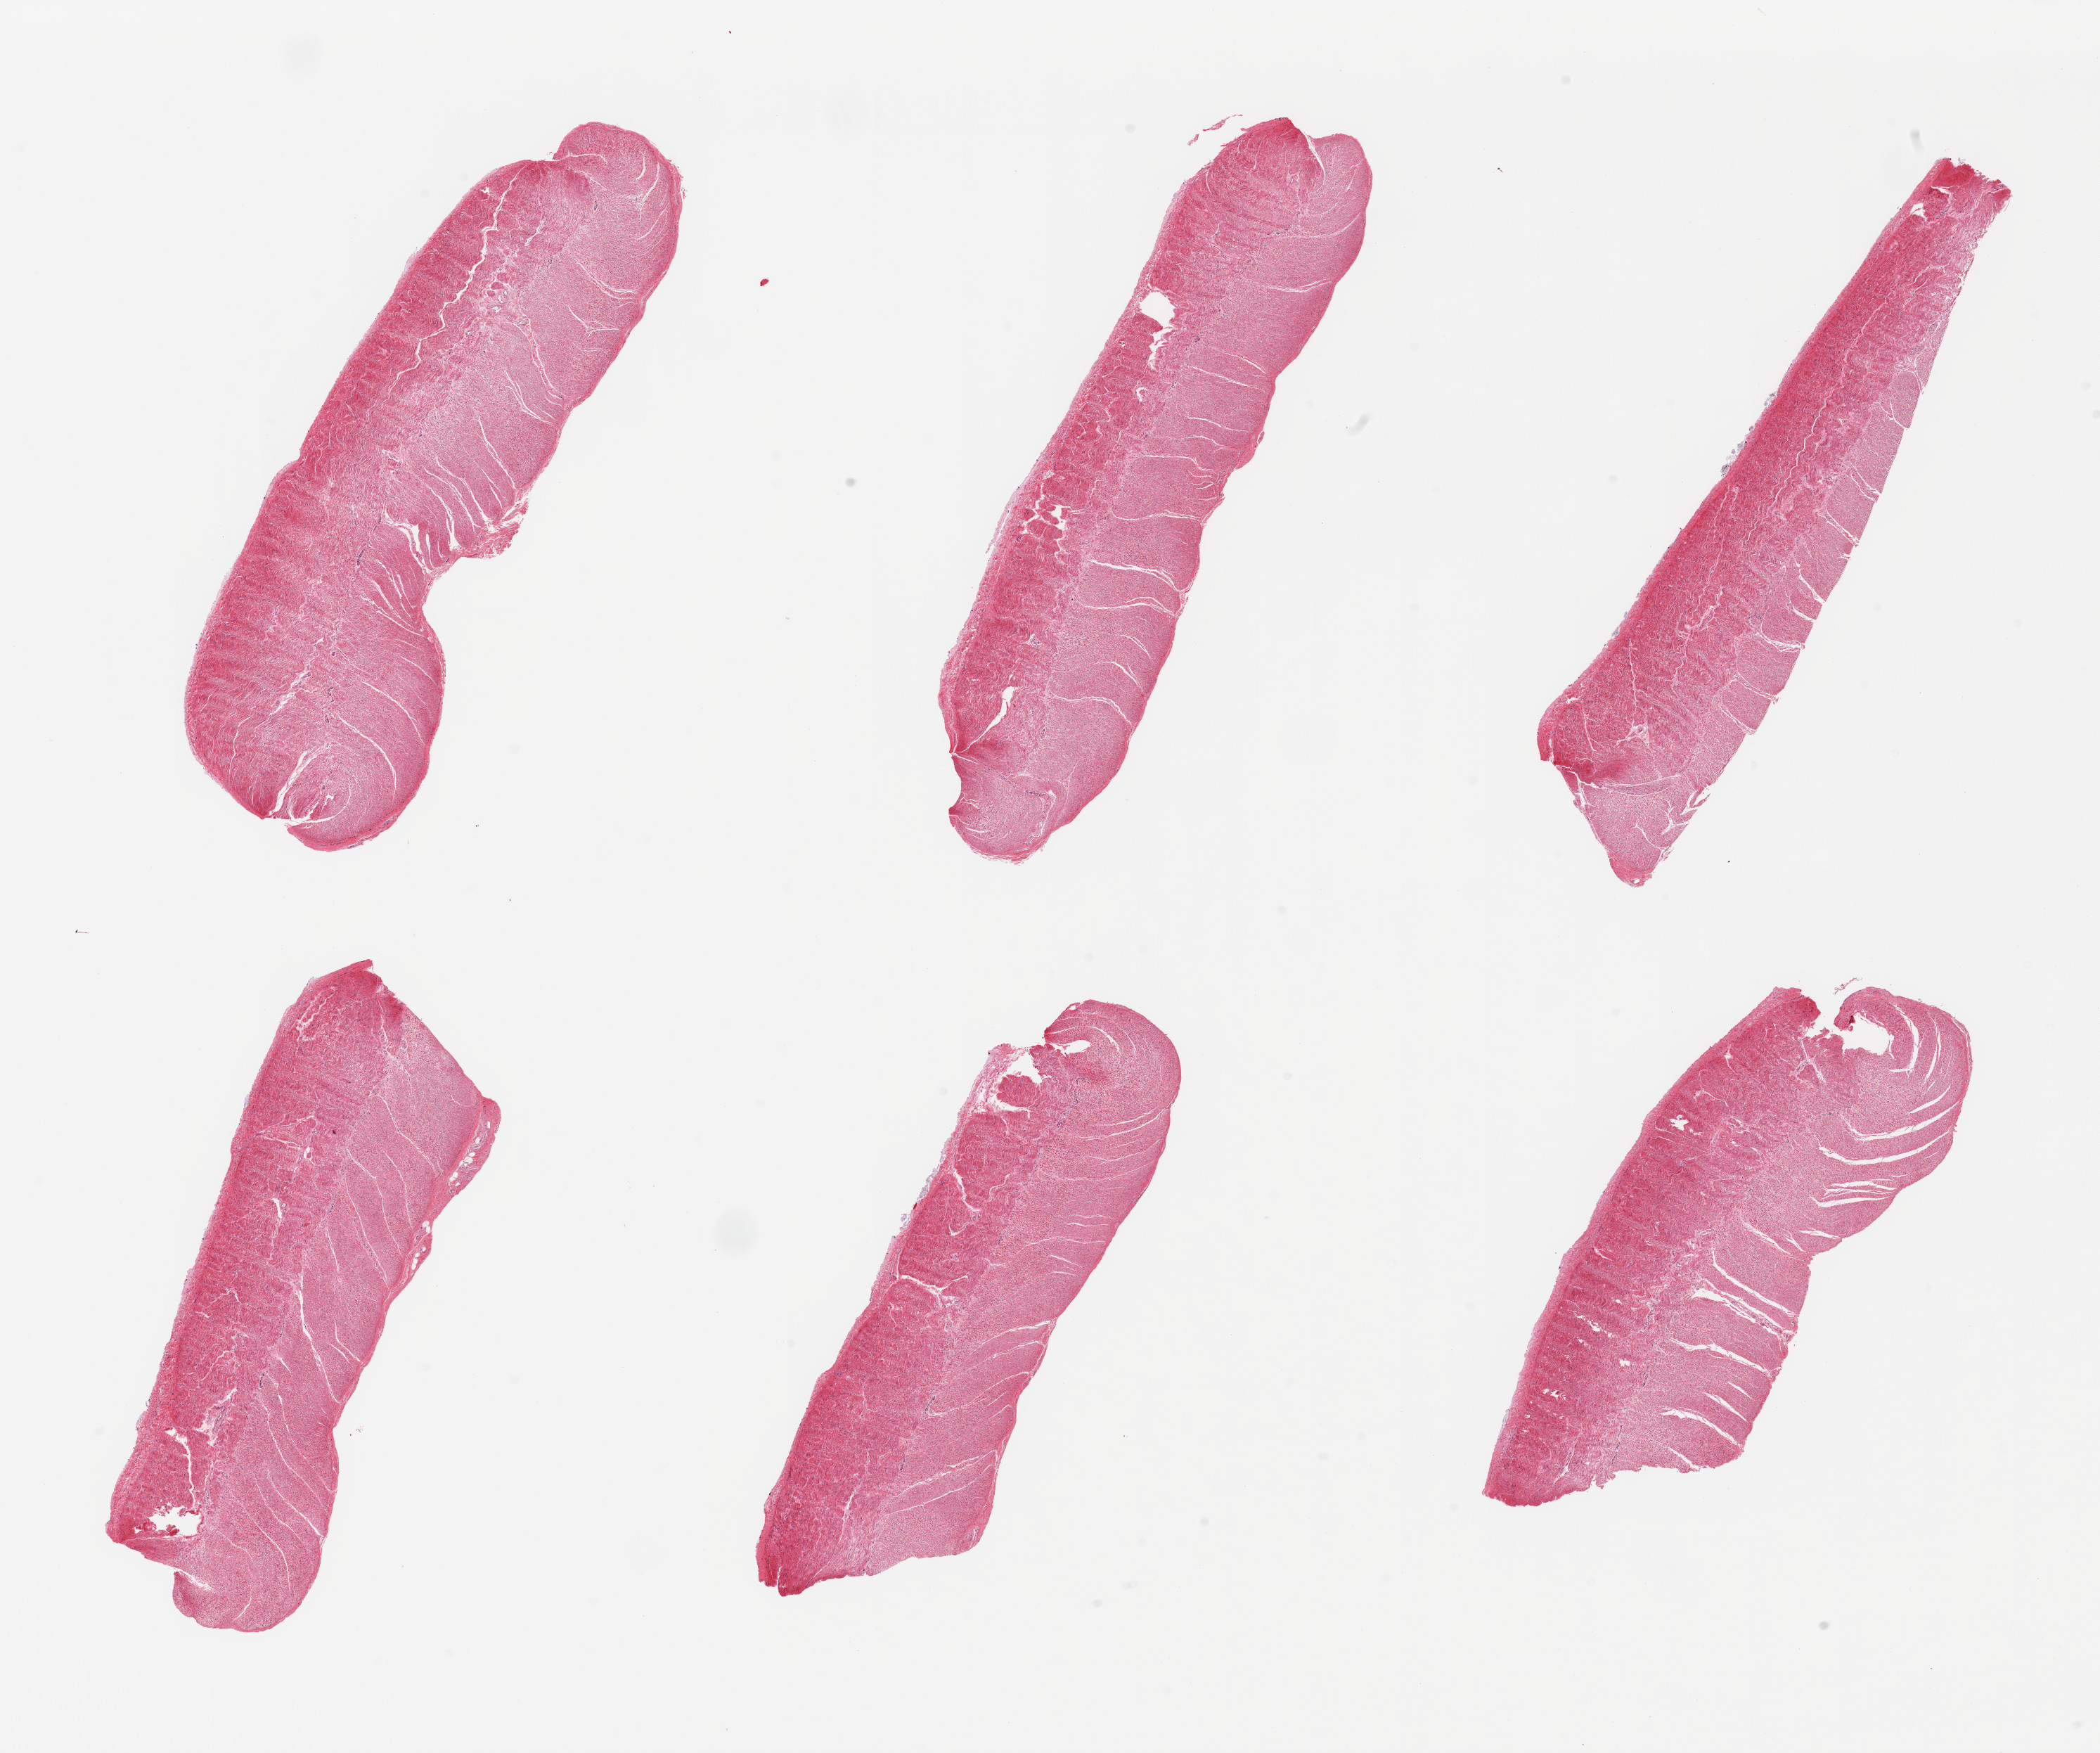
Digitized H&E-stained section, a low-resolution overview of the entire scanned area, about 23.6 x 19.7 mm. PAXgene-fixed, paraffin-embedded tissue. Target tissue: sigmoid colon. Donor tissue sample.
• reviewer comment on this tissue sample: 6 pieces; well trimmed target muscularis